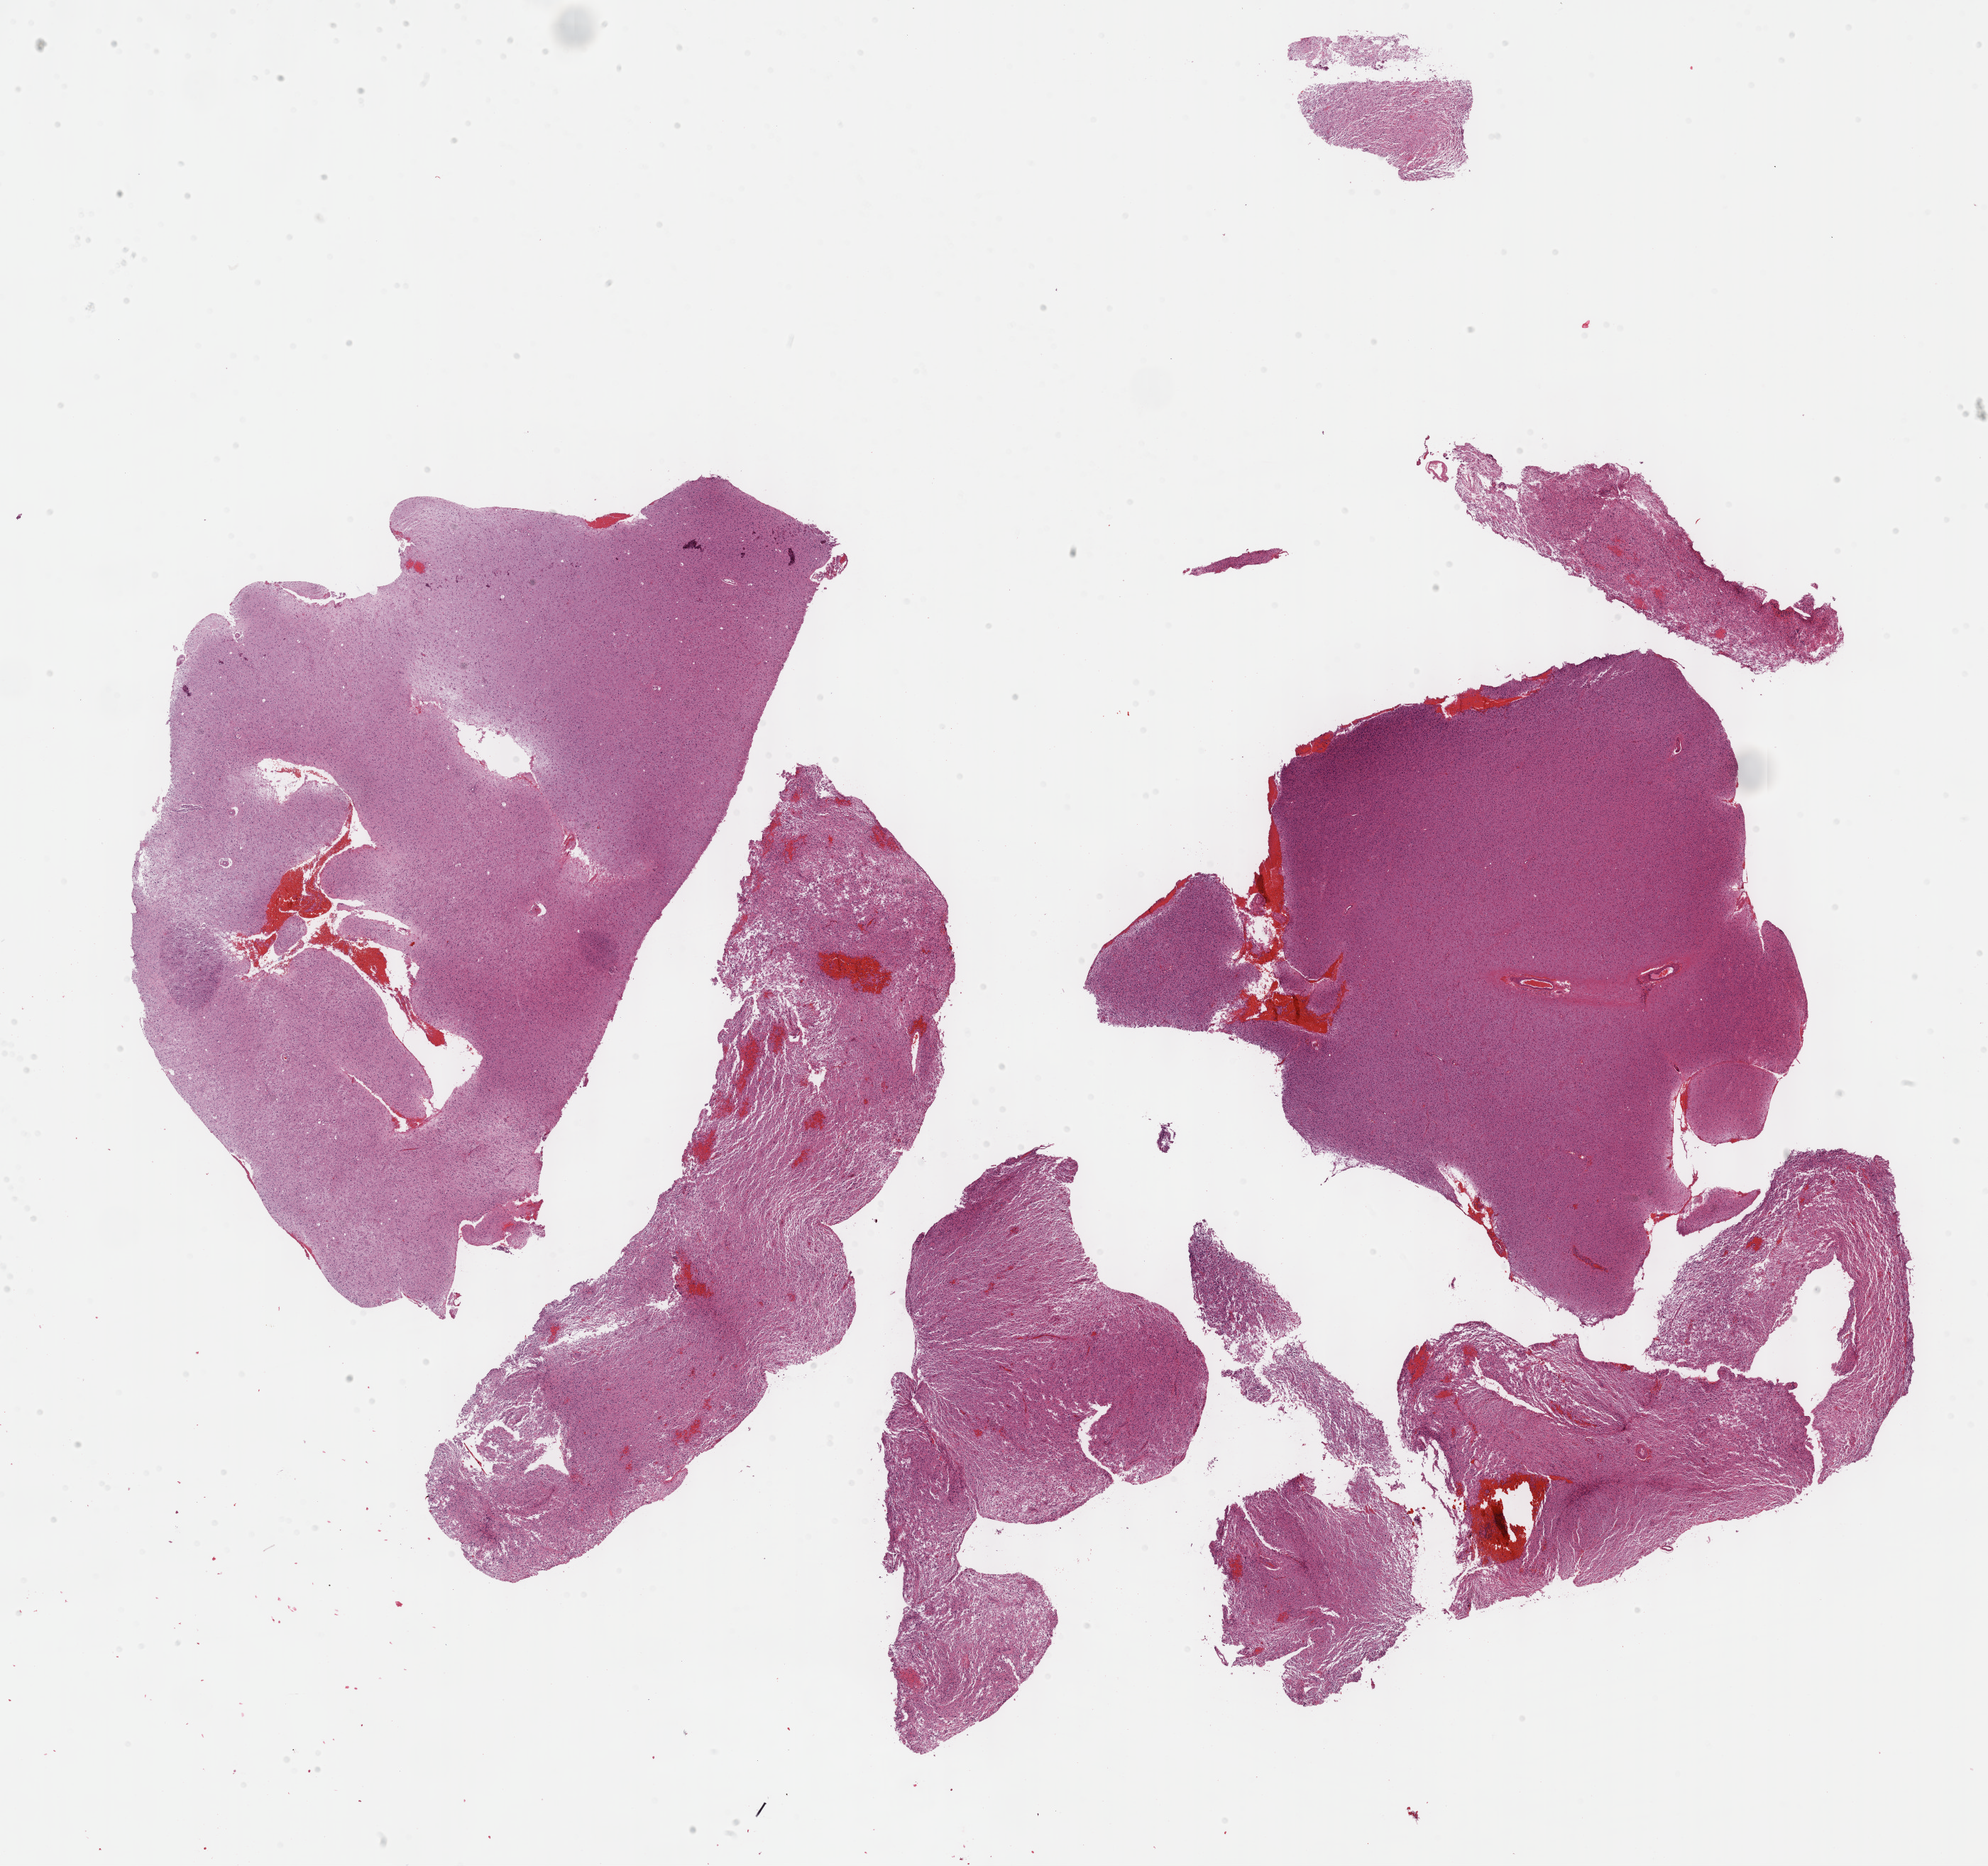
Digitized Hematoxylin and eosin (H&E) stained tissue section (whole slide), low-resolution overview of the scanned area, about 22.7 x 21.3 mm (slide scanned at 40x). Formalin-fixed paraffin-embedded (FFPE) diagnostic section. Sample: primary tumour, brain. Patient: female, age at initial diagnosis 29 years. Histologic grade: G3 (poorly differentiated).
Pathologic diagnosis: Astrocytoma, anaplastic (cerebrum).